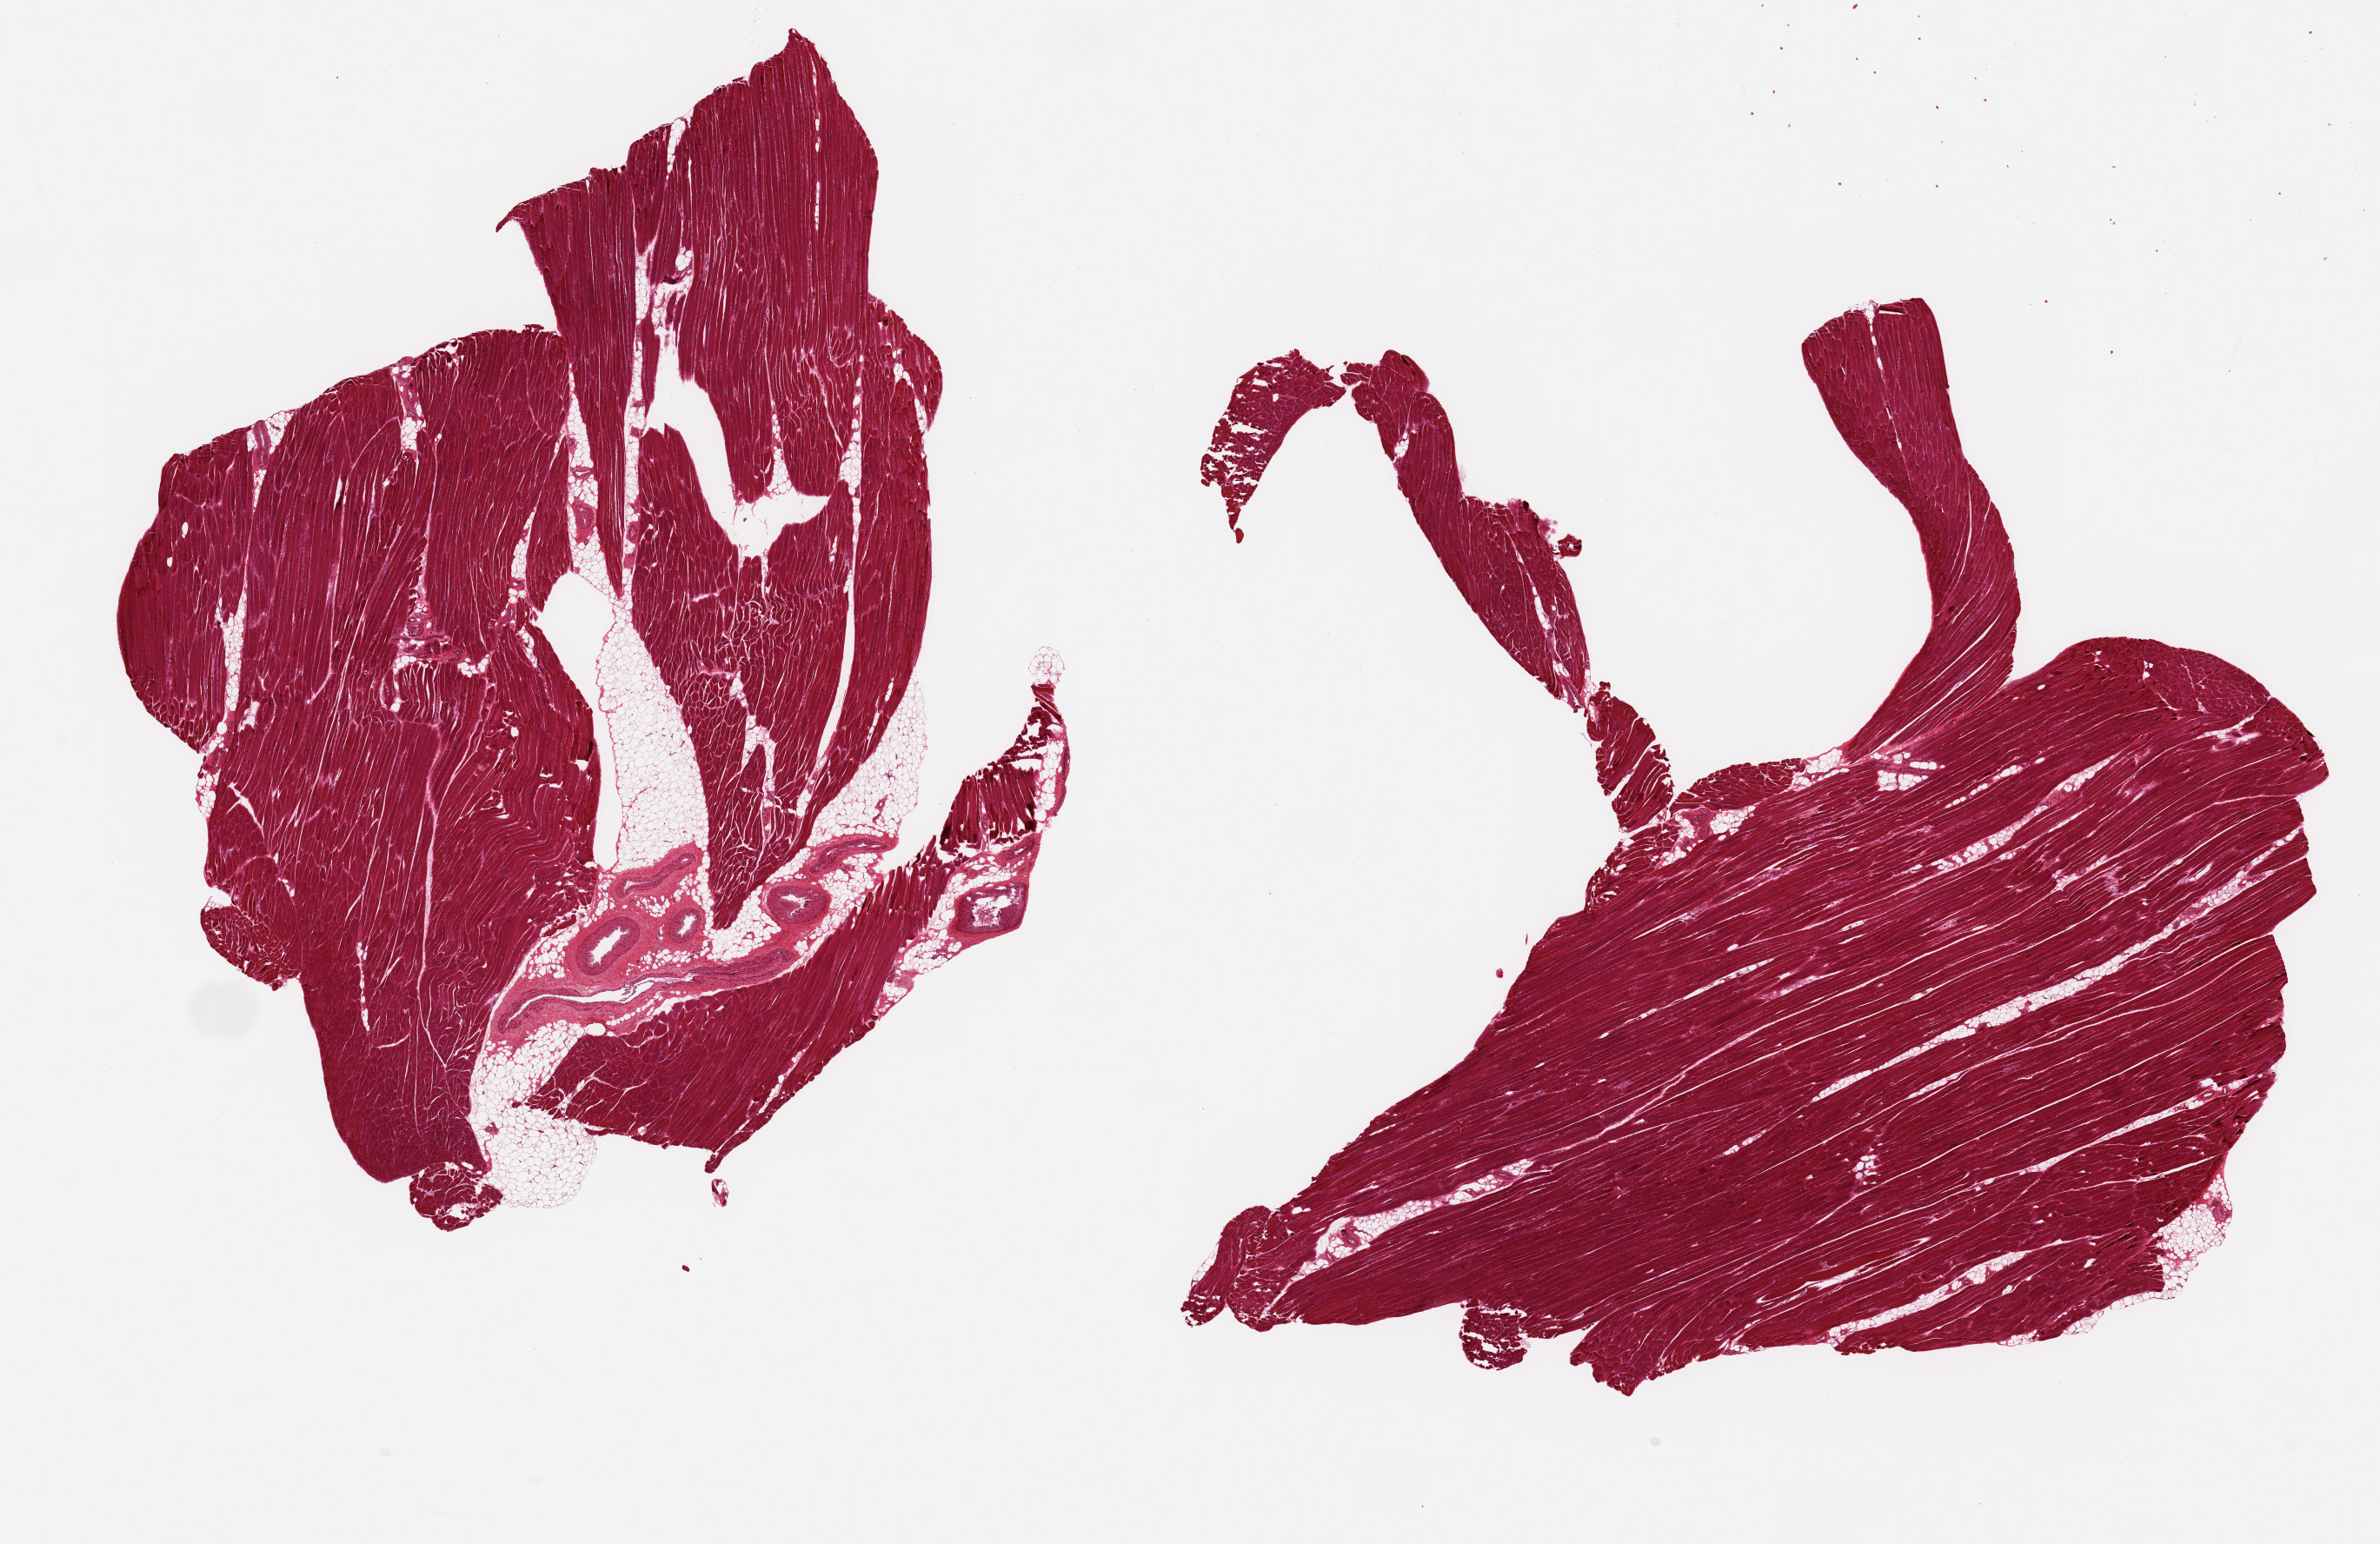
Digitized hematoxylin and eosin (H&E)-stained section, brightfield — shown as a low-resolution overview of the whole scanned area (about 21.7 x 14.0 mm), PAXgene-fixed paraffin-embedded (PFPE) section, target tissue: skeletal muscle, tissue donor sample. Male donor.
Review note (as recorded): 2 ~11x6mm aliquot; <5% interstitial adipose tissue, clean specimens.